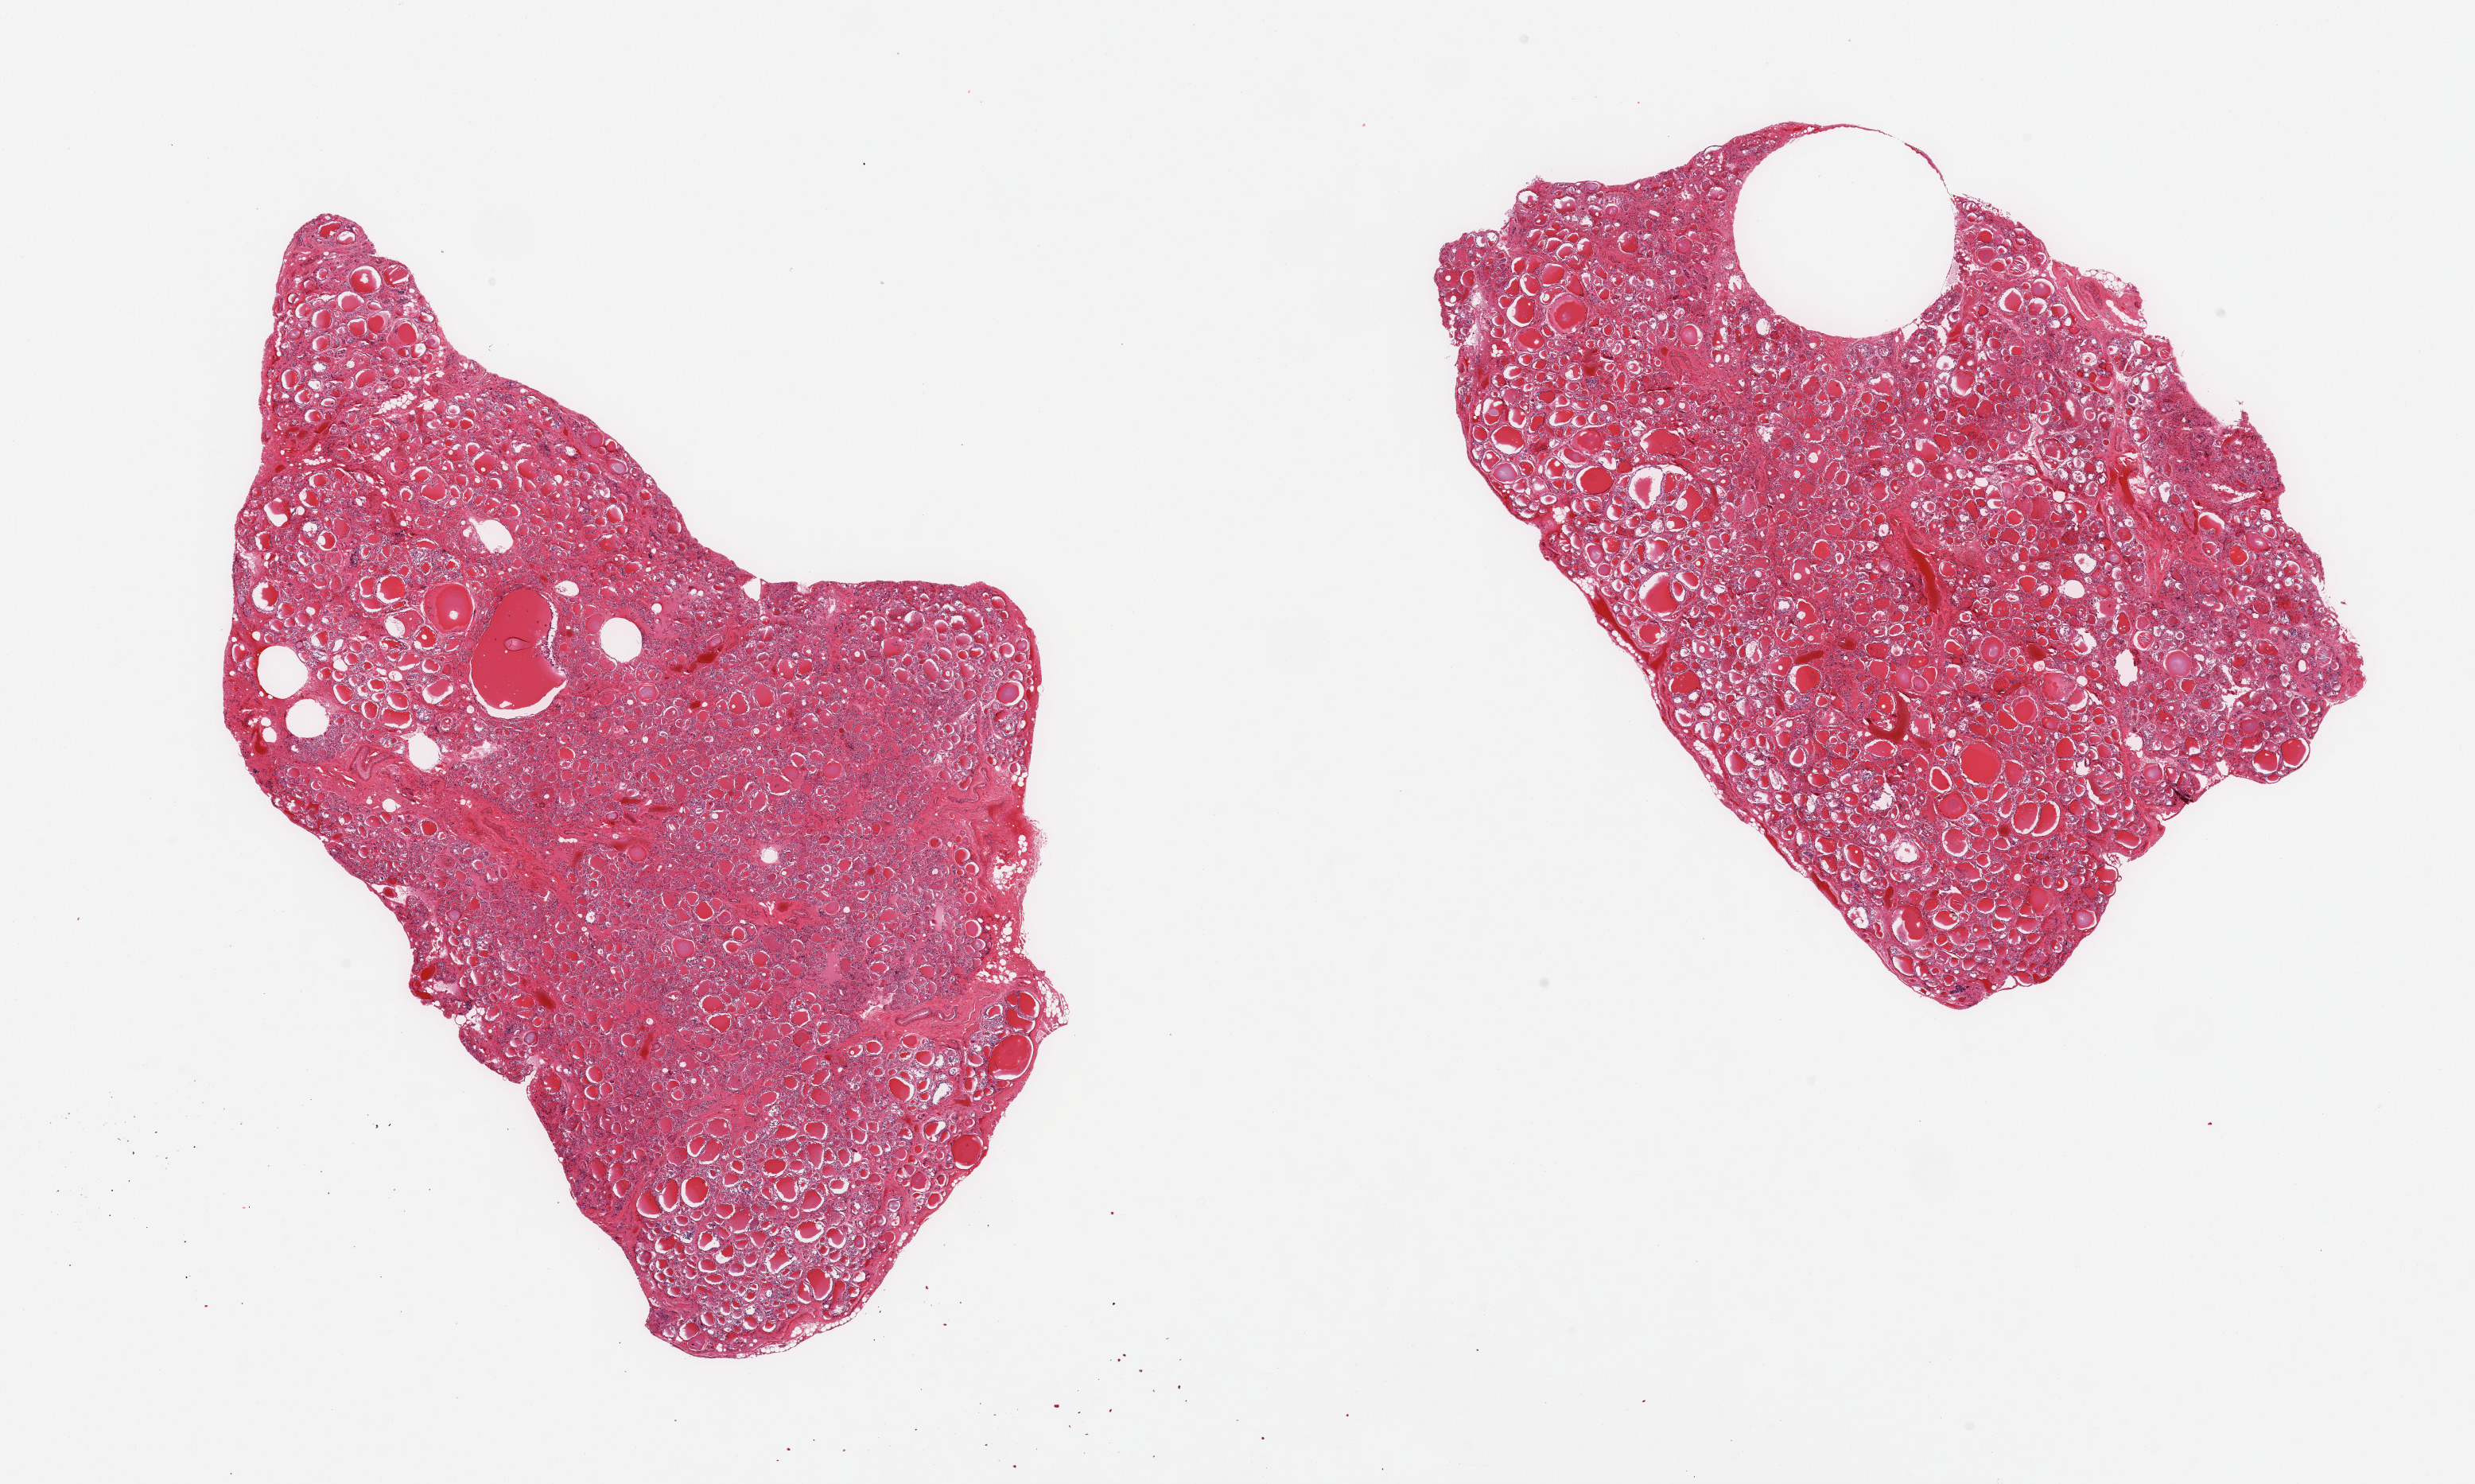
Digitized hematoxylin and eosin (H&E)-stained section, brightfield, low-resolution overview of the scanned area, about 24.6 x 14.8 mm; PAXgene-fixed paraffin-embedded (PFPE) section; sampled site (target tissue): thyroid; tissue donor sample. Donor: female.
- review note (as recorded): 2 pieces